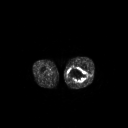
FDG PET of an extremity soft-tissue mass (from a PET/CT study), one axial slice. Position 228 of 267 along the scan axis. 3.27 mm slice thickness. 128 × 128 image matrix, field of view 700 × 700 mm. Male patient, age 44 years. From the clinical record (not read from this slice): histological type: undifferentiated pleomorphic liposarcoma; grade: high; site of the primary tumour: left thigh.
Structures marked on this image (expert contour drawn on MRI and transferred to this co-registered scan by the dataset authors):
- gross tumour volume including surrounding oedema: bounding box (x1, y1, x2, y2) in pixels: (67, 67, 87, 83)
- gross tumour volume (mass): (67, 67, 87, 83)